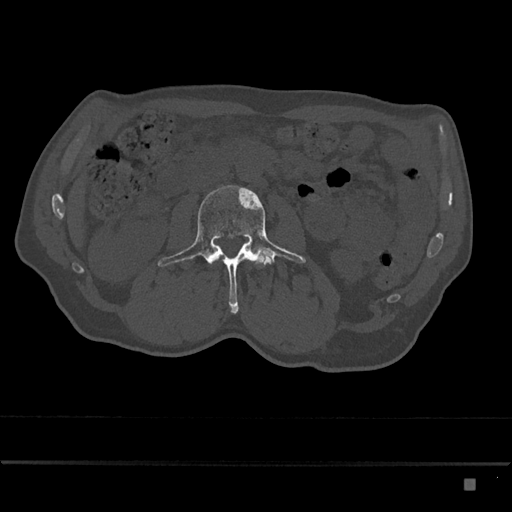
CT including the spine, one axial slice. Bone window (W 1800 / L 400 HU). 0.5 mm slice thickness. 512 × 512 image matrix, field of view 390 × 390 mm. Patient: male, 72 years. From the clinical record (not read from this slice): primary cancer: prostate.
Outlined on this slice (semi-automatic segmentation, software-assisted and operator-edited):
- L3 vertebra: box from (x=158, y=185) to (x=306, y=314) px